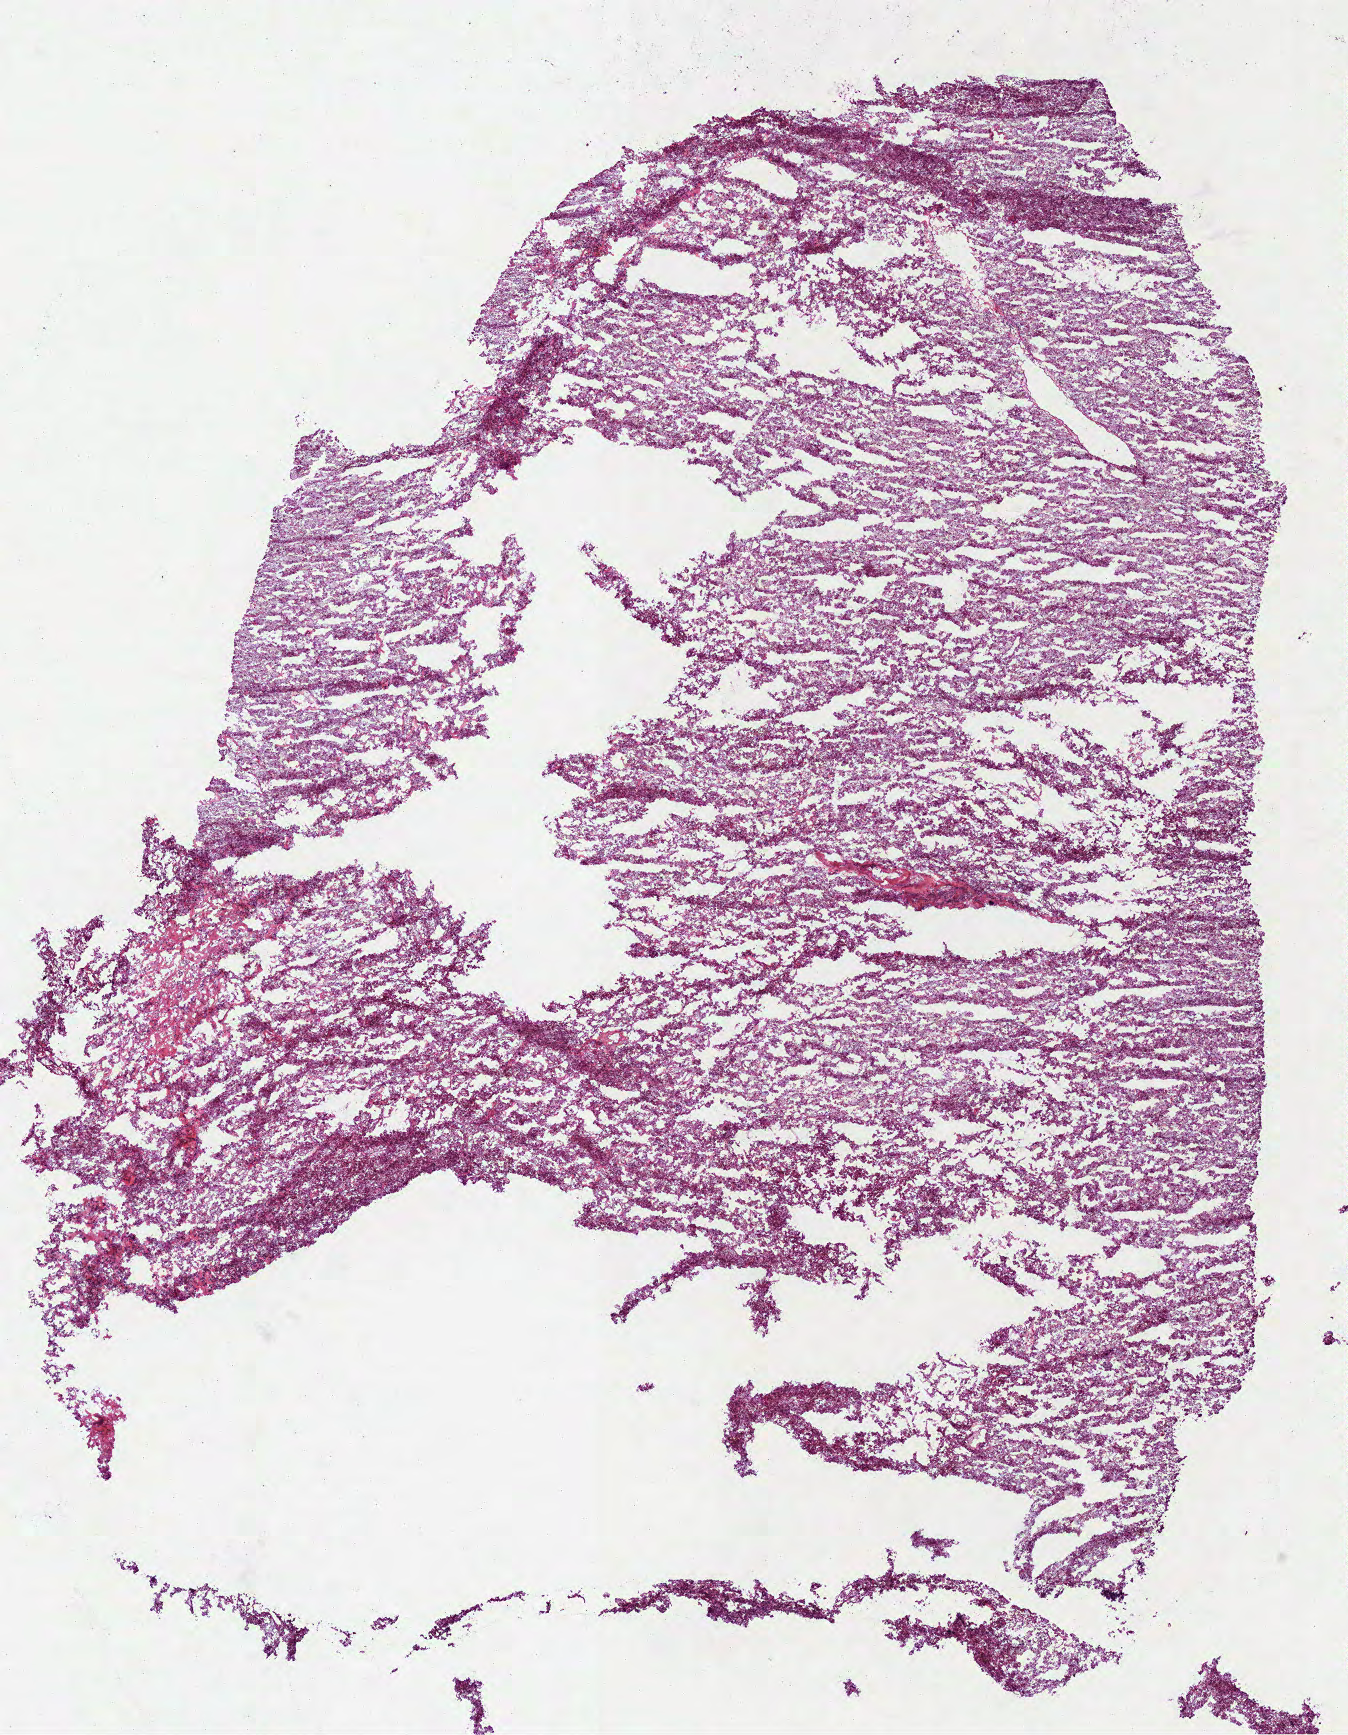
Whole-slide histology image, Hematoxylin and eosin (H&E) stained — shown as a low-resolution overview of the whole scanned area (about 10.9 x 14.0 mm, acquisition: 40x scan). Frozen section. Sample: primary tumour, kidney. Male patient; age at initial diagnosis 53 years. Pathologist review of this section (percent, as recorded): tumour cells 100%, tumour nuclei 80%, normal cells 0%, stromal cells 0%, necrosis 0%. Infiltration values recorded for this section: lymphocyte infiltration 0%, monocyte infiltration 15%, neutrophil infiltration 0%.
Histologic diagnosis: Renal cell carcinoma, chromophobe type. AJCC pathologic stage: I (6th edition).